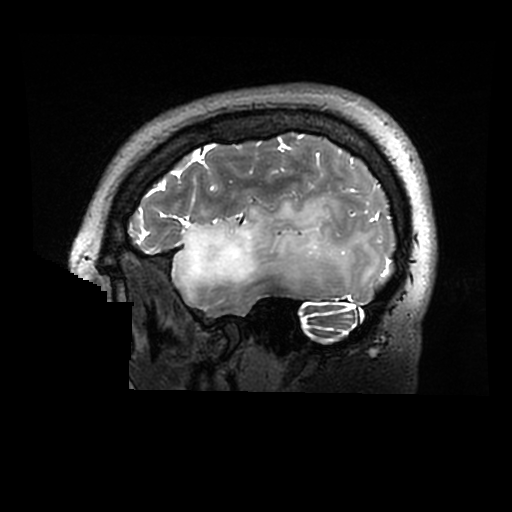
Brain MRI from a brain-tumour surgery series, one sagittal slice. Position 234 of 320 along the scan axis. 512 × 512 image matrix, field of view 240 × 240 mm. From the clinical record (not read from this slice): histopathology: Astrocytoma; WHO grade: 2; IDH mutation: yes.
Structures marked on this image (outlined manually by an expert reader):
- tumour: bounding box (x1, y1, x2, y2) in pixels: (172, 197, 379, 298)